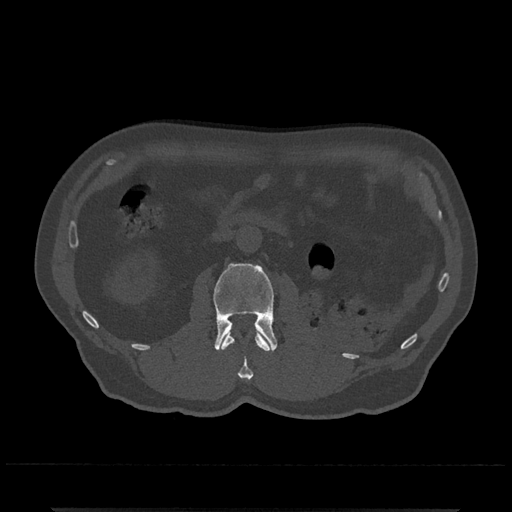
CT including the spine, one axial slice. Position 312 of 797 along the scan axis. Reconstruction kernel Br40s/3. 120 kVp. Bone window (W 1800 / L 400 HU). 512 × 512 image matrix, field of view 393 × 393 mm. Patient: male, 67 years. From the clinical record (not read from this slice): primary cancer: prostate.
Outlined on this slice (semi-automatically segmented with operator editing):
- L1 vertebra: bounding box (x1, y1, x2, y2) in pixels: (221, 330, 270, 380)
- L2 vertebra: (213, 263, 278, 352)